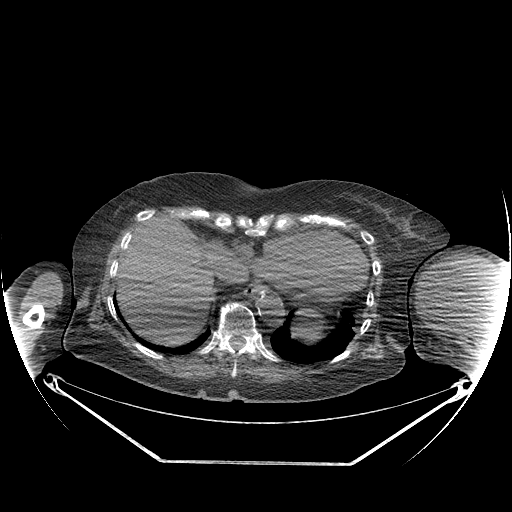
CT of an extremity soft-tissue mass (from a PET/CT study), one axial slice; position 146 of 267 along the scan axis; reconstruction kernel STANDARD; 140 kVp; soft-tissue window (W 400 / L 40 HU); 3.75 mm slice thickness; 512 × 512 image matrix, field of view 500 × 500 mm. Female patient. From the clinical record (not read from this slice): histological type: pleiomorphic leiomyosarcoma; grade: high; site of the primary tumour: left biceps.
Structures marked on this image (expert contour drawn on MRI and transferred to this co-registered scan by the dataset authors):
- gross tumour volume including surrounding oedema: bounding box [x1, y1, x2, y2] px = [422, 256, 499, 323]
- gross tumour volume (mass): [422, 256, 499, 320]